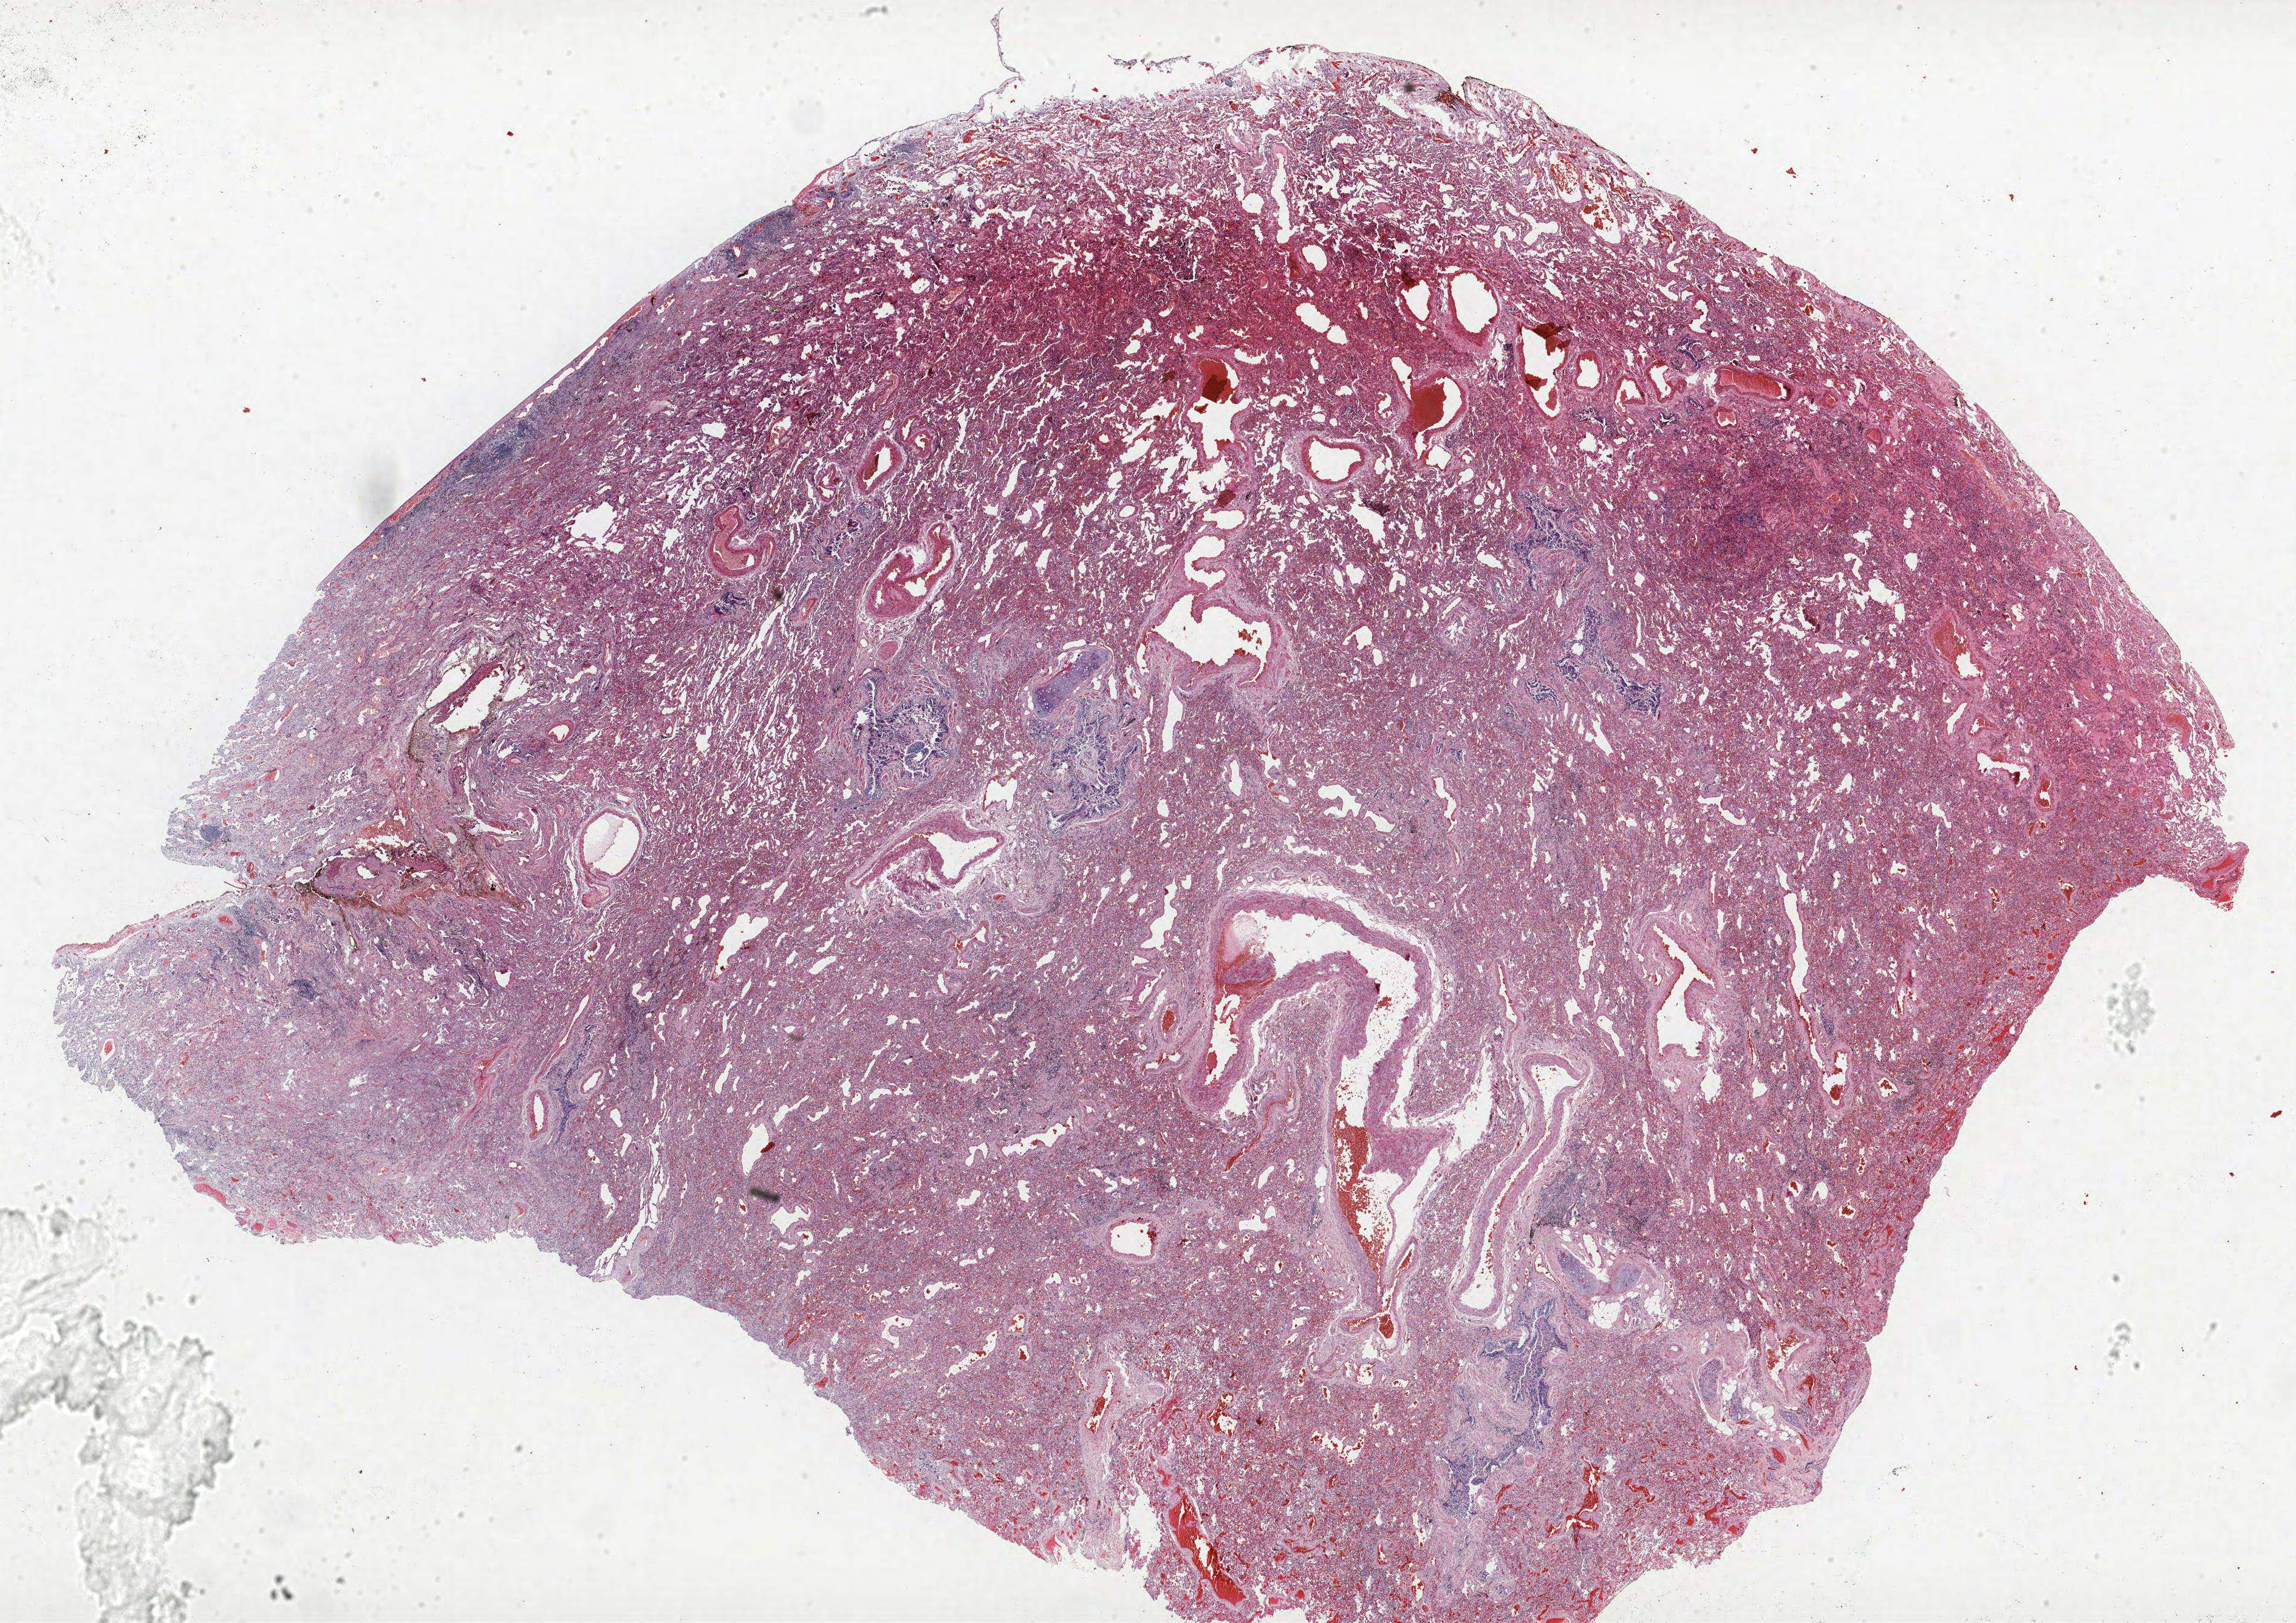
Hematoxylin and eosin (H&E) stained whole-slide image — a low-resolution overview of the entire scanned area, about 30.2 x 21.4 mm. FFPE section. Lung. Male, age 65 at enrolment. Grade: poorly differentiated (G3).
Stage (AJCC 6th edition): IA. Primary tumour location (clinical record): right lower lobe. Tumour size (pathology): 10 mm. Participant's lung-cancer diagnosis: Adenocarcinoma, NOS.